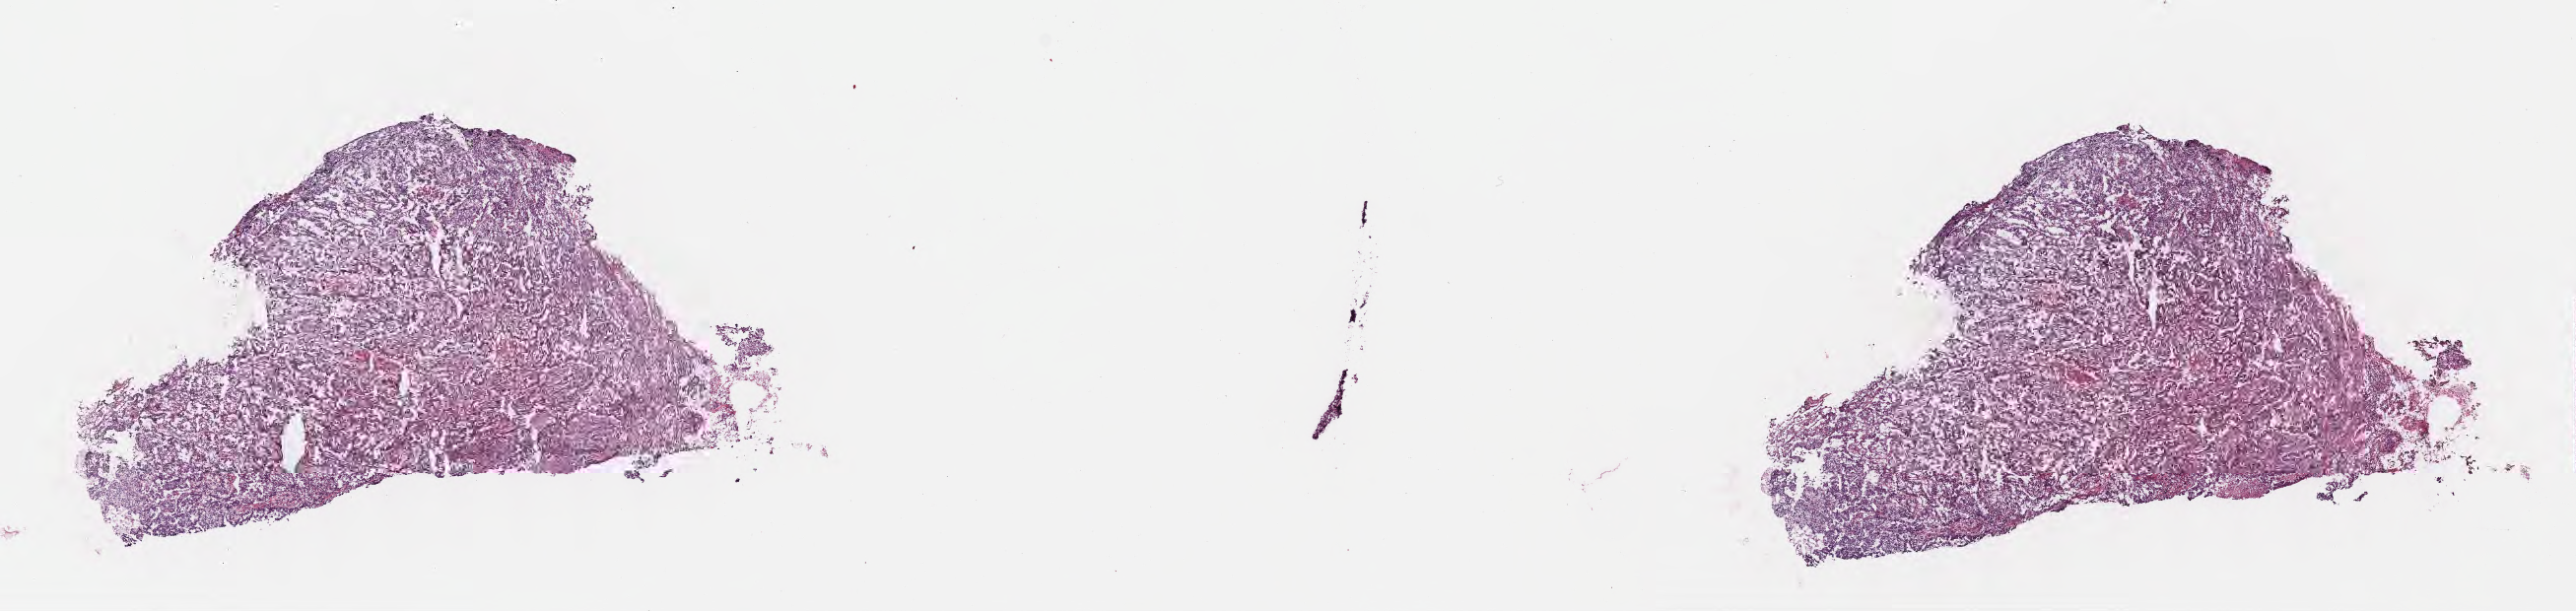
Whole-slide image, hematoxylin and eosin (H&E) stain, shown as a low-resolution overview of the whole scanned area (about 21.1 x 5.0 mm); frozen section (tissue freezing medium); primary tumor; site: lower lobe of right lung. Male patient, age 71 years. Composition of this section per pathologist review: tumor cells 65%, tumor nuclei 65%, stromal cells 33%, necrosis 0%, normal cells 2%. Infiltration values recorded for this section: lymphocyte infiltration 7%, monocyte infiltration 4%, neutrophil infiltration 8%.
Histologic diagnosis: Clear cell adenocarcinoma, NOS. Section: top of the tissue portion. AJCC pathologic stage: Stage IIIA.